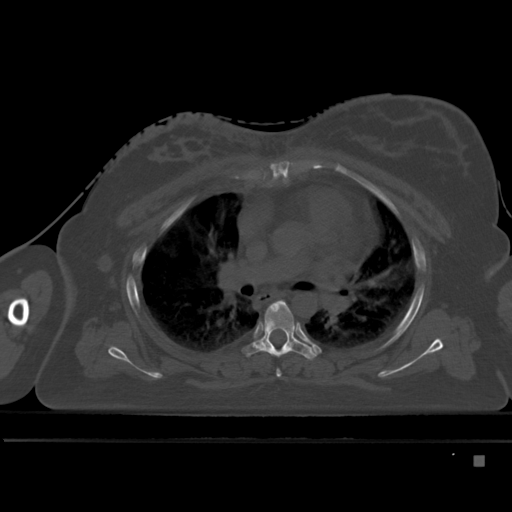
CT including the spine, one axial slice. Slice 322 of 495 in the series (ordered by position). Bone window (W 1800 / L 400 HU). 1.5 mm slice thickness. 512 × 512 image matrix, field of view 404 × 404 mm. Female patient, age 33 years. From the clinical record (not read from this slice): primary cancer: breast; vertebrae with lytic lesions (as recorded): T1.
Annotated regions visible in this slice (semi-automatic segmentation, software-assisted and operator-edited):
- T4 vertebra: bounding box [x1, y1, x2, y2] px = [276, 370, 281, 377]
- T5 vertebra: [243, 300, 317, 359]